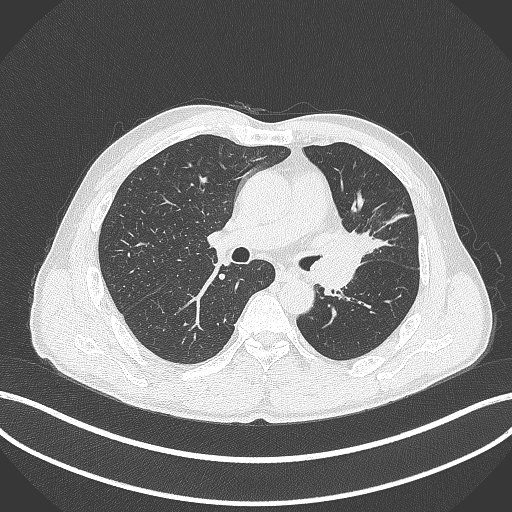
Chest CT, one axial slice. Reconstruction kernel B70f. 120 kVp. Lung window (W 1500 / L -600 HU). 512 × 512 image matrix, field of view 400 × 400 mm. Patient: male, 57 years. Case-level facts recorded for this patient, not image findings: clinical TNM (as recorded): T2b N0 M0.
Outlined on this slice (bounding box drawn by a radiologist):
- lung tumour (recorded histology: squamous cell carcinoma): box from (x=316, y=227) to (x=374, y=267) px